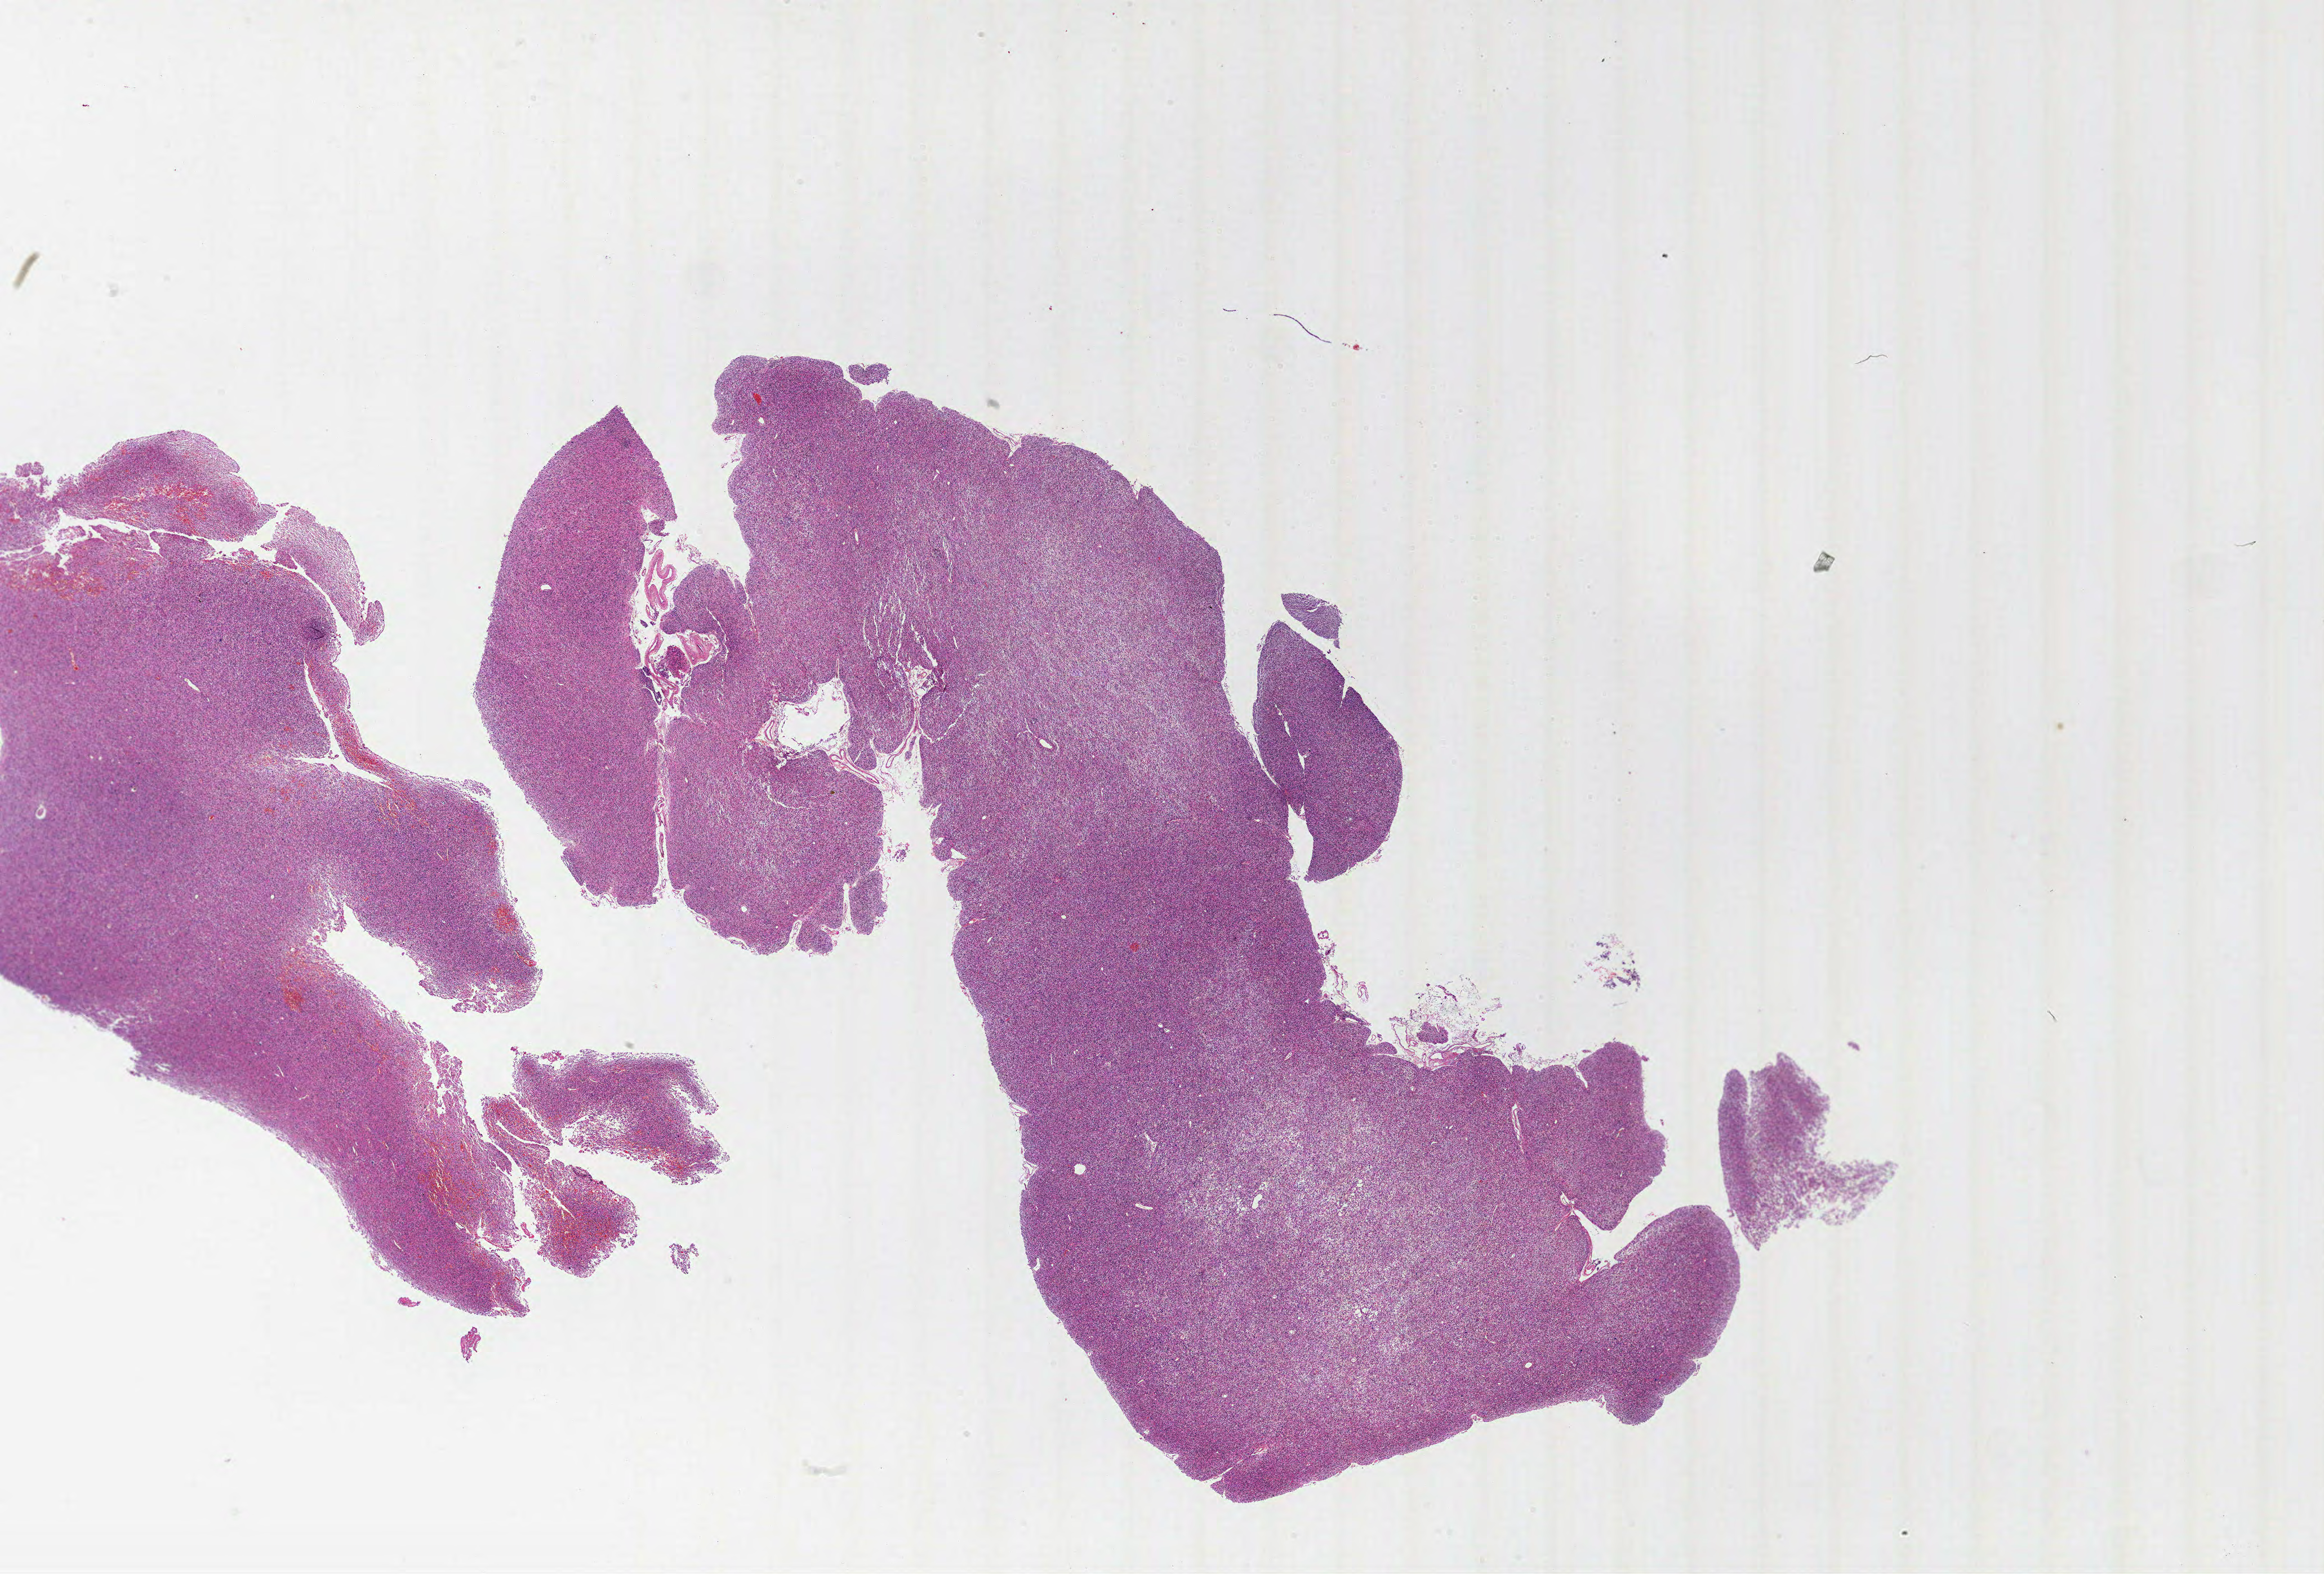
Hematoxylin and eosin (H&E) stained whole-slide image — whole scanned area (about 33.0 x 22.3 mm, from a 20x scan) shown as a low-resolution overview, formalin-fixed paraffin-embedded (FFPE) diagnostic section, primary tumour sample from the brain. Male, age 63 years at initial diagnosis.
• histologic diagnosis: Glioblastoma